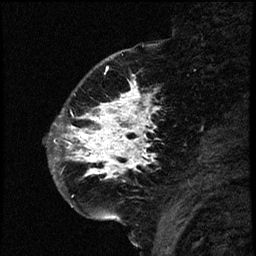
Breast MRI (dynamic contrast-enhanced), one sagittal slice; slice 20 of 66 in the series (ordered by position); dynamic contrast-enhanced study with each time point stored as its own series, time point 2 of 3 at this slice position (early post-contrast, ordered by acquisition time); 1.5 T; TE 4.2 ms, TR 17.6 ms; 256 × 256 image matrix, field of view 200 × 200 mm. Female patient. From the clinical record (not read from this slice): setting: breast cancer imaged before/during neoadjuvant chemotherapy; receptor status: HER2-positive.
Outlined on this slice (semi-automatic segmentation, software-assisted and operator-edited):
- analysis volume of interest (the breast-tissue region the enhancement analysis was run in; not a lesion): bounding box [x1, y1, x2, y2] px = [52, 69, 177, 209]
- tumour enhancement mask (voxels above the 100 % enhancement threshold inside the analysis volume of interest): [53, 82, 158, 179]